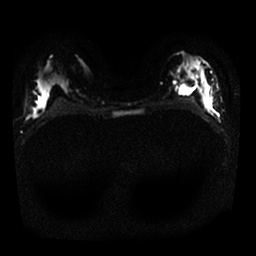
Breast MRI, one axial slice; position 13 of 25 along the scan axis; diffusion-weighted series; image 2 of 4 stored at this slice position (different b-values; order by instance number); 1.5 T; 256 × 256 image matrix. Female patient.
Annotated regions visible in this slice (outlined manually by an expert reader):
- tumour on diffusion-weighted imaging: bounding box (x1, y1, x2, y2) in pixels: (202, 85, 211, 107)